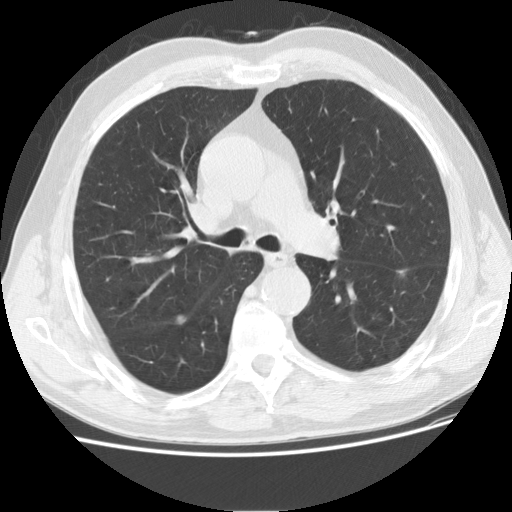
Low-dose screening chest CT, axial slice; second screening round (one year after baseline); lung window (W 1500 / L -600 HU); 512 × 512 image matrix, field of view 360 × 360 mm. Male participant, aged 73 years at enrolment.
Lesion marked by an expert reader, bounding box (x1, y1, x2, y2) in pixels: (374, 257, 422, 296). Screening reader's record for this exam (one nodule recorded; not confirmed to be the boxed lesion): non-calcified nodule or mass ≥4 mm, left lower lobe, 16 × 10 mm, smooth margins, soft tissue attenuation, pre-existing on the prior screen: yes; interval growth: yes. Official screen result: positive, other. Lung cancer was diagnosed 76 days after this screen: adenocarcinoma, NOS, left lower lobe, poorly differentiated (G3), stage IIA (AJCC 6th edition), 12 mm at pathology.